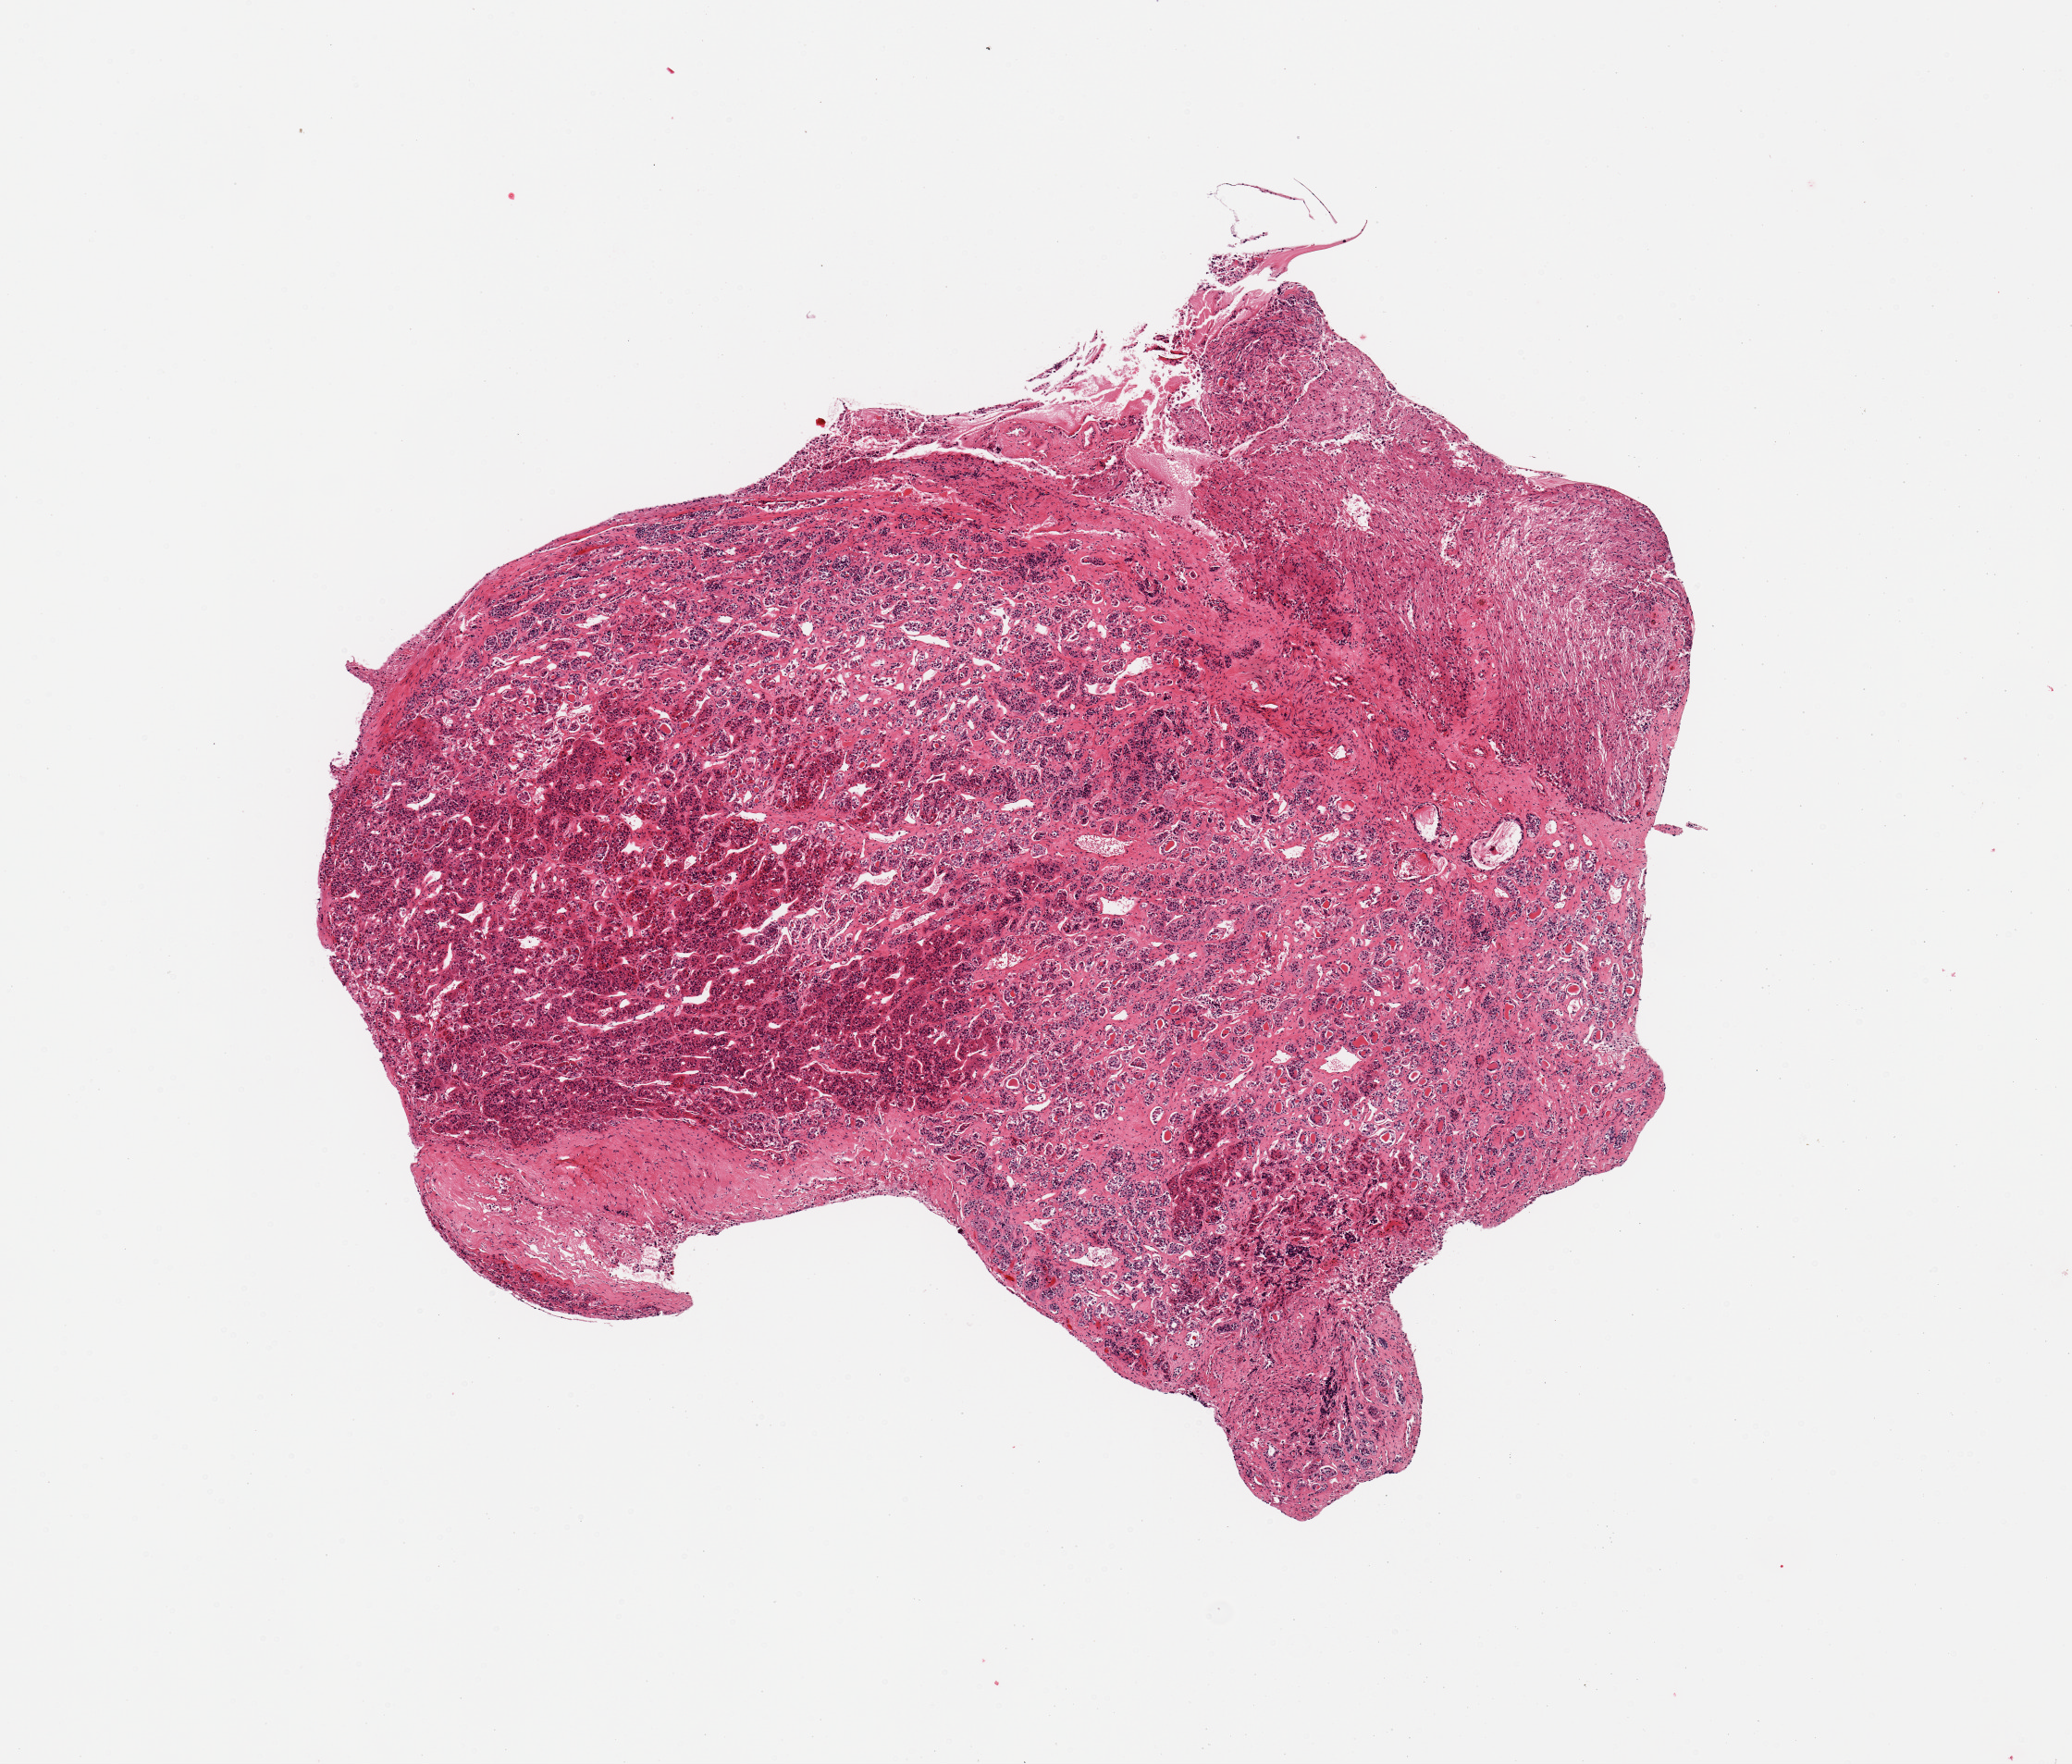
Digitized hematoxylin and eosin (H&E)-stained section, a low-resolution overview of the entire scanned area, about 8.9 x 7.5 mm (from a 20x scan); PAXgene-fixed, paraffin-embedded tissue; section of pituitary (target tissue); tissue donor sample. Male donor.
Pathologist's review note for this sample: 1 piece; adenohypophysis and neurohypophysis present.